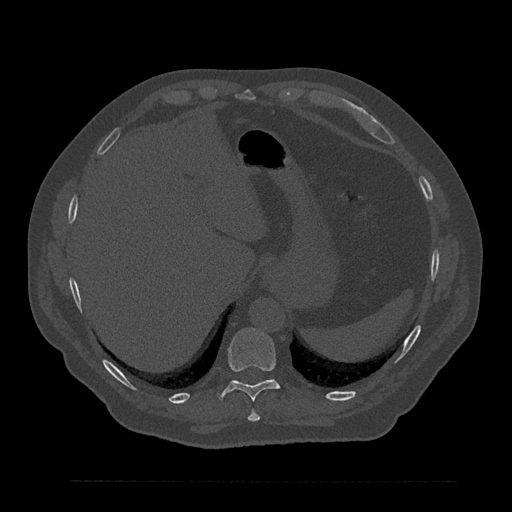
CT including the spine, one axial slice; slice 344 of 797 in the series (ordered by position); reconstruction kernel Br40s/3; 120 kVp; bone window (W 1800 / L 400 HU); 0.5 mm slice thickness; 512 × 512 image matrix. Male patient, age 61 years. Case-level facts recorded for this patient, not image findings: primary cancer: prostate.
Outlined on this slice (semi-automatic segmentation, software-assisted and operator-edited):
- T10 vertebra: bounding box [x1, y1, x2, y2] px = [219, 328, 280, 401]
- T9 vertebra: [248, 410, 260, 422]